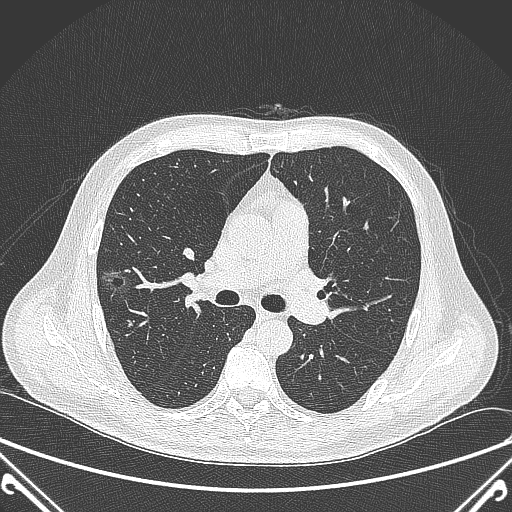
Chest CT, one axial slice. Position 224 of 360 along the scan axis. 120 kVp. Lung window (W 1500 / L -600 HU). 1 mm slice thickness. 512 × 512 image matrix, field of view 380 × 380 mm. Patient: male, 64 years. Case-level facts recorded for this patient, not image findings: clinical TNM (as recorded): T1c N0 M0.
Outlined on this slice (rectangle marked by the reading radiologist):
- lung tumour (recorded histology: adenocarcinoma): bounding box <95,260,134,295> (left, top, right, bottom; pixels)